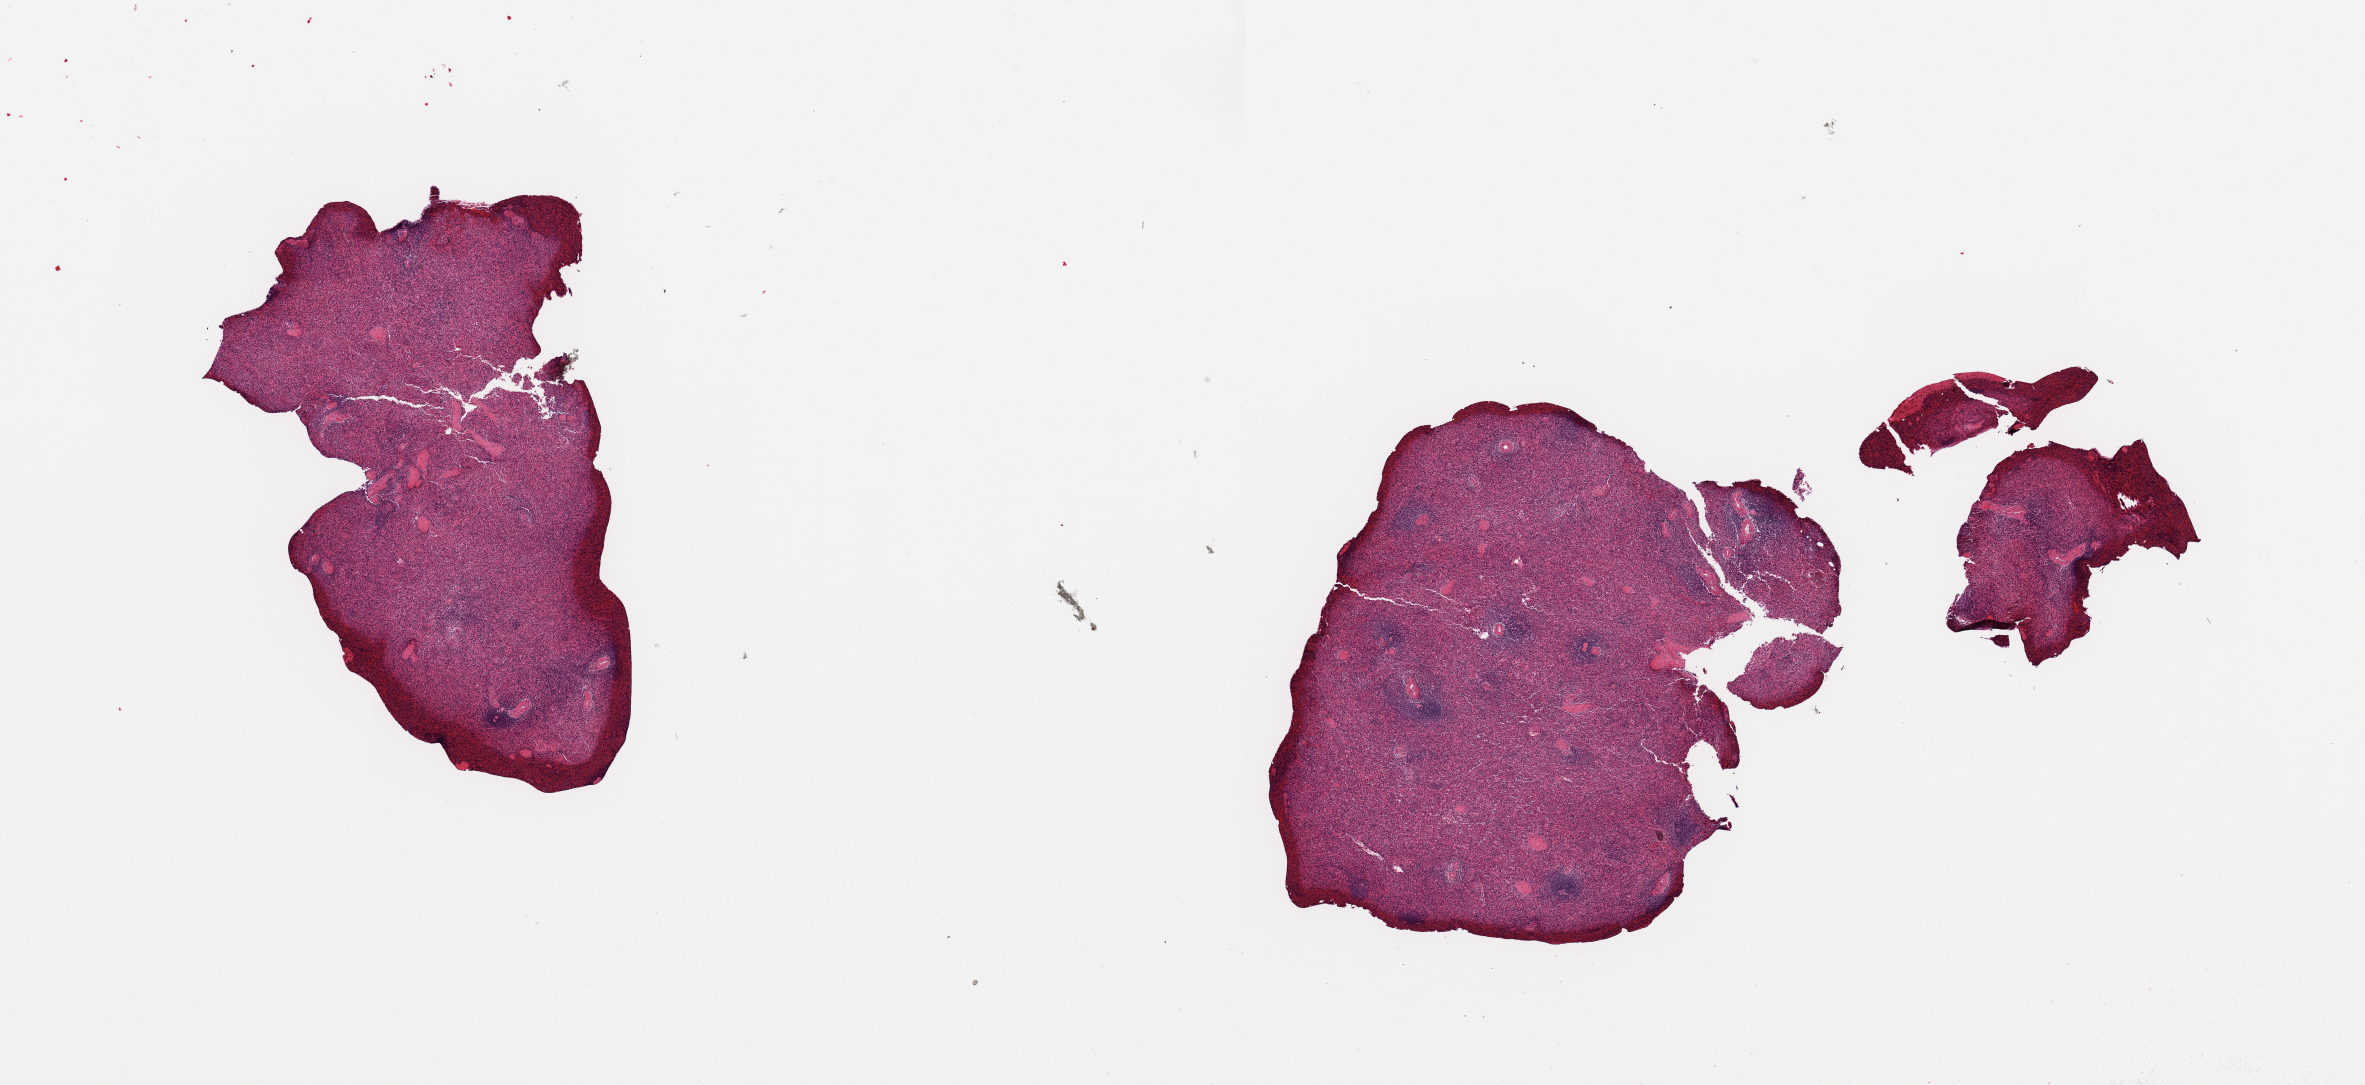
Whole-slide image, hematoxylin and eosin (H&E) stain, shown as a low-resolution overview of the whole scanned area (about 18.7 x 8.6 mm); PAXgene-fixed paraffin-embedded (PFPE) section; sampled site (target tissue): spleen; tissue donor sample. Male donor.
* reviewer comment on this tissue sample: 2 partially fragmented pieces; up to 0.28mm artefactual outer rim possibly due to drying or incorrect fixation